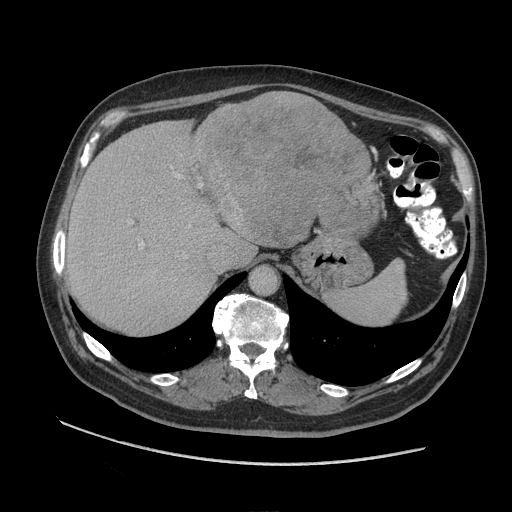
Contrast-enhanced abdominal CT (liver protocol), one axial slice. Position 70 of 109 along the scan axis. 140 kVp. Soft-tissue window (W 400 / L 40 HU). 2.5 mm slice thickness. 512 × 512 image matrix, field of view 420 × 420 mm. Case-level facts recorded for this patient, not image findings: diagnosis: hepatocellular carcinoma (patient treated with transarterial chemoembolisation; whether this scan precedes or follows treatment is not stated here); TNM stage (as recorded): Stage-I; Child-Pugh class: A.
Outlined on this slice (semi-automatically segmented with operator editing):
- abdominal aorta: bounding box [x1, y1, x2, y2] px = [250, 267, 278, 294]
- liver parenchyma outside the tumour (the mass and vessels are separate outlines, so this box may not span the whole liver): [66, 107, 372, 334]
- mass: [199, 90, 370, 247]
- liver vessels: [140, 166, 202, 248]